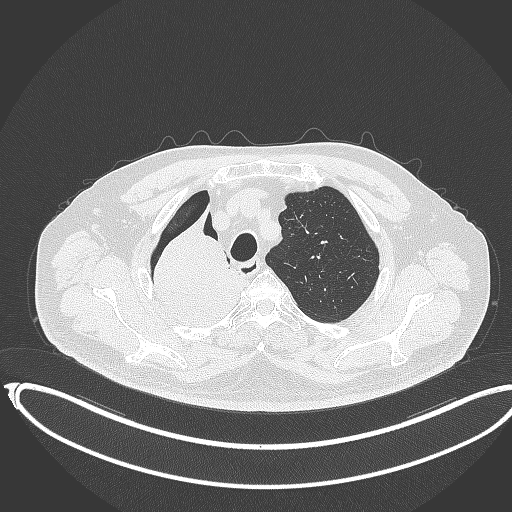
Chest CT, one axial slice; slice 300 of 403 in the series (ordered by position); reconstruction kernel B70f; lung window (W 1500 / L -600 HU); 512 × 512 image matrix, field of view 436 × 436 mm. Patient: male, 68 years. Case-level facts recorded for this patient, not image findings: clinical TNM (as recorded): T2a N0 M0.
Outlined on this slice (rectangle marked by the reading radiologist):
- lung tumour (recorded histology: adenocarcinoma): bounding box (x1, y1, x2, y2) in pixels: (138, 204, 242, 330)